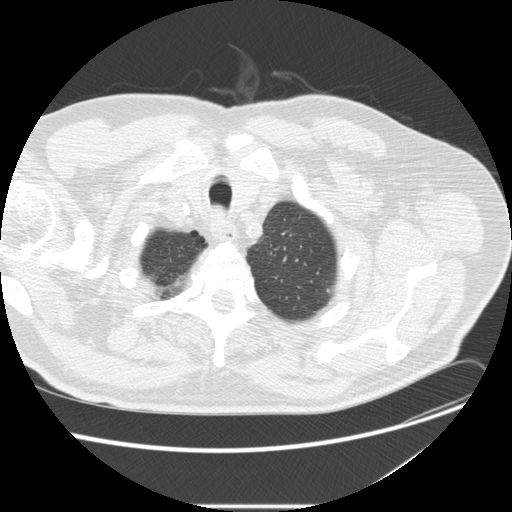
Axial slice from a low-dose chest CT screening exam; baseline screening round; lung window (W 1500 / L -600 HU); standard (soft-tissue) reconstruction kernel (STANDARD); slice 32 of 263 in the series. Male participant, aged 73 years at enrolment.
Lesion marked by an expert reader, bounding box [x1, y1, x2, y2] px = [315, 280, 338, 297]. Screening reader's record for this exam: no non-calcified nodule ≥4 mm recorded. Official screen result: negative screen, minor abnormalities not suspicious for lung cancer.